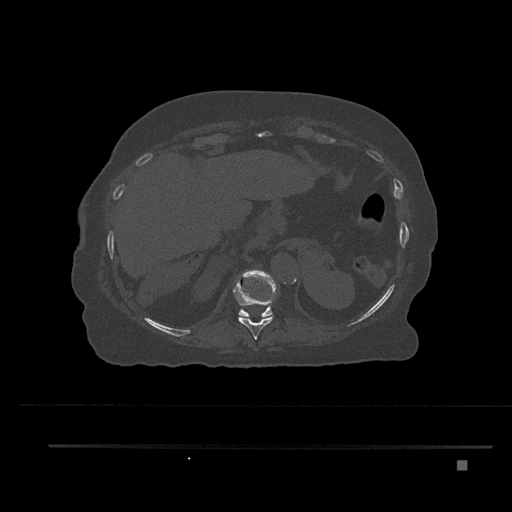
CT including the spine, one axial slice. Slice 340 of 797 in the series (ordered by position). Reconstruction kernel Br40s/3. Bone window (W 1800 / L 400 HU). 512 × 512 image matrix, field of view 437 × 437 mm. Patient: female, 76 years. Case-level facts recorded for this patient, not image findings: primary cancer: lung; vertebrae with lytic lesions (as recorded): T11, L3.
Outlined on this slice (semi-automatic segmentation, software-assisted and operator-edited):
- T10 vertebra: bounding box <233,279,276,340> (left, top, right, bottom; pixels)
- T11 vertebra: <238,270,277,317>